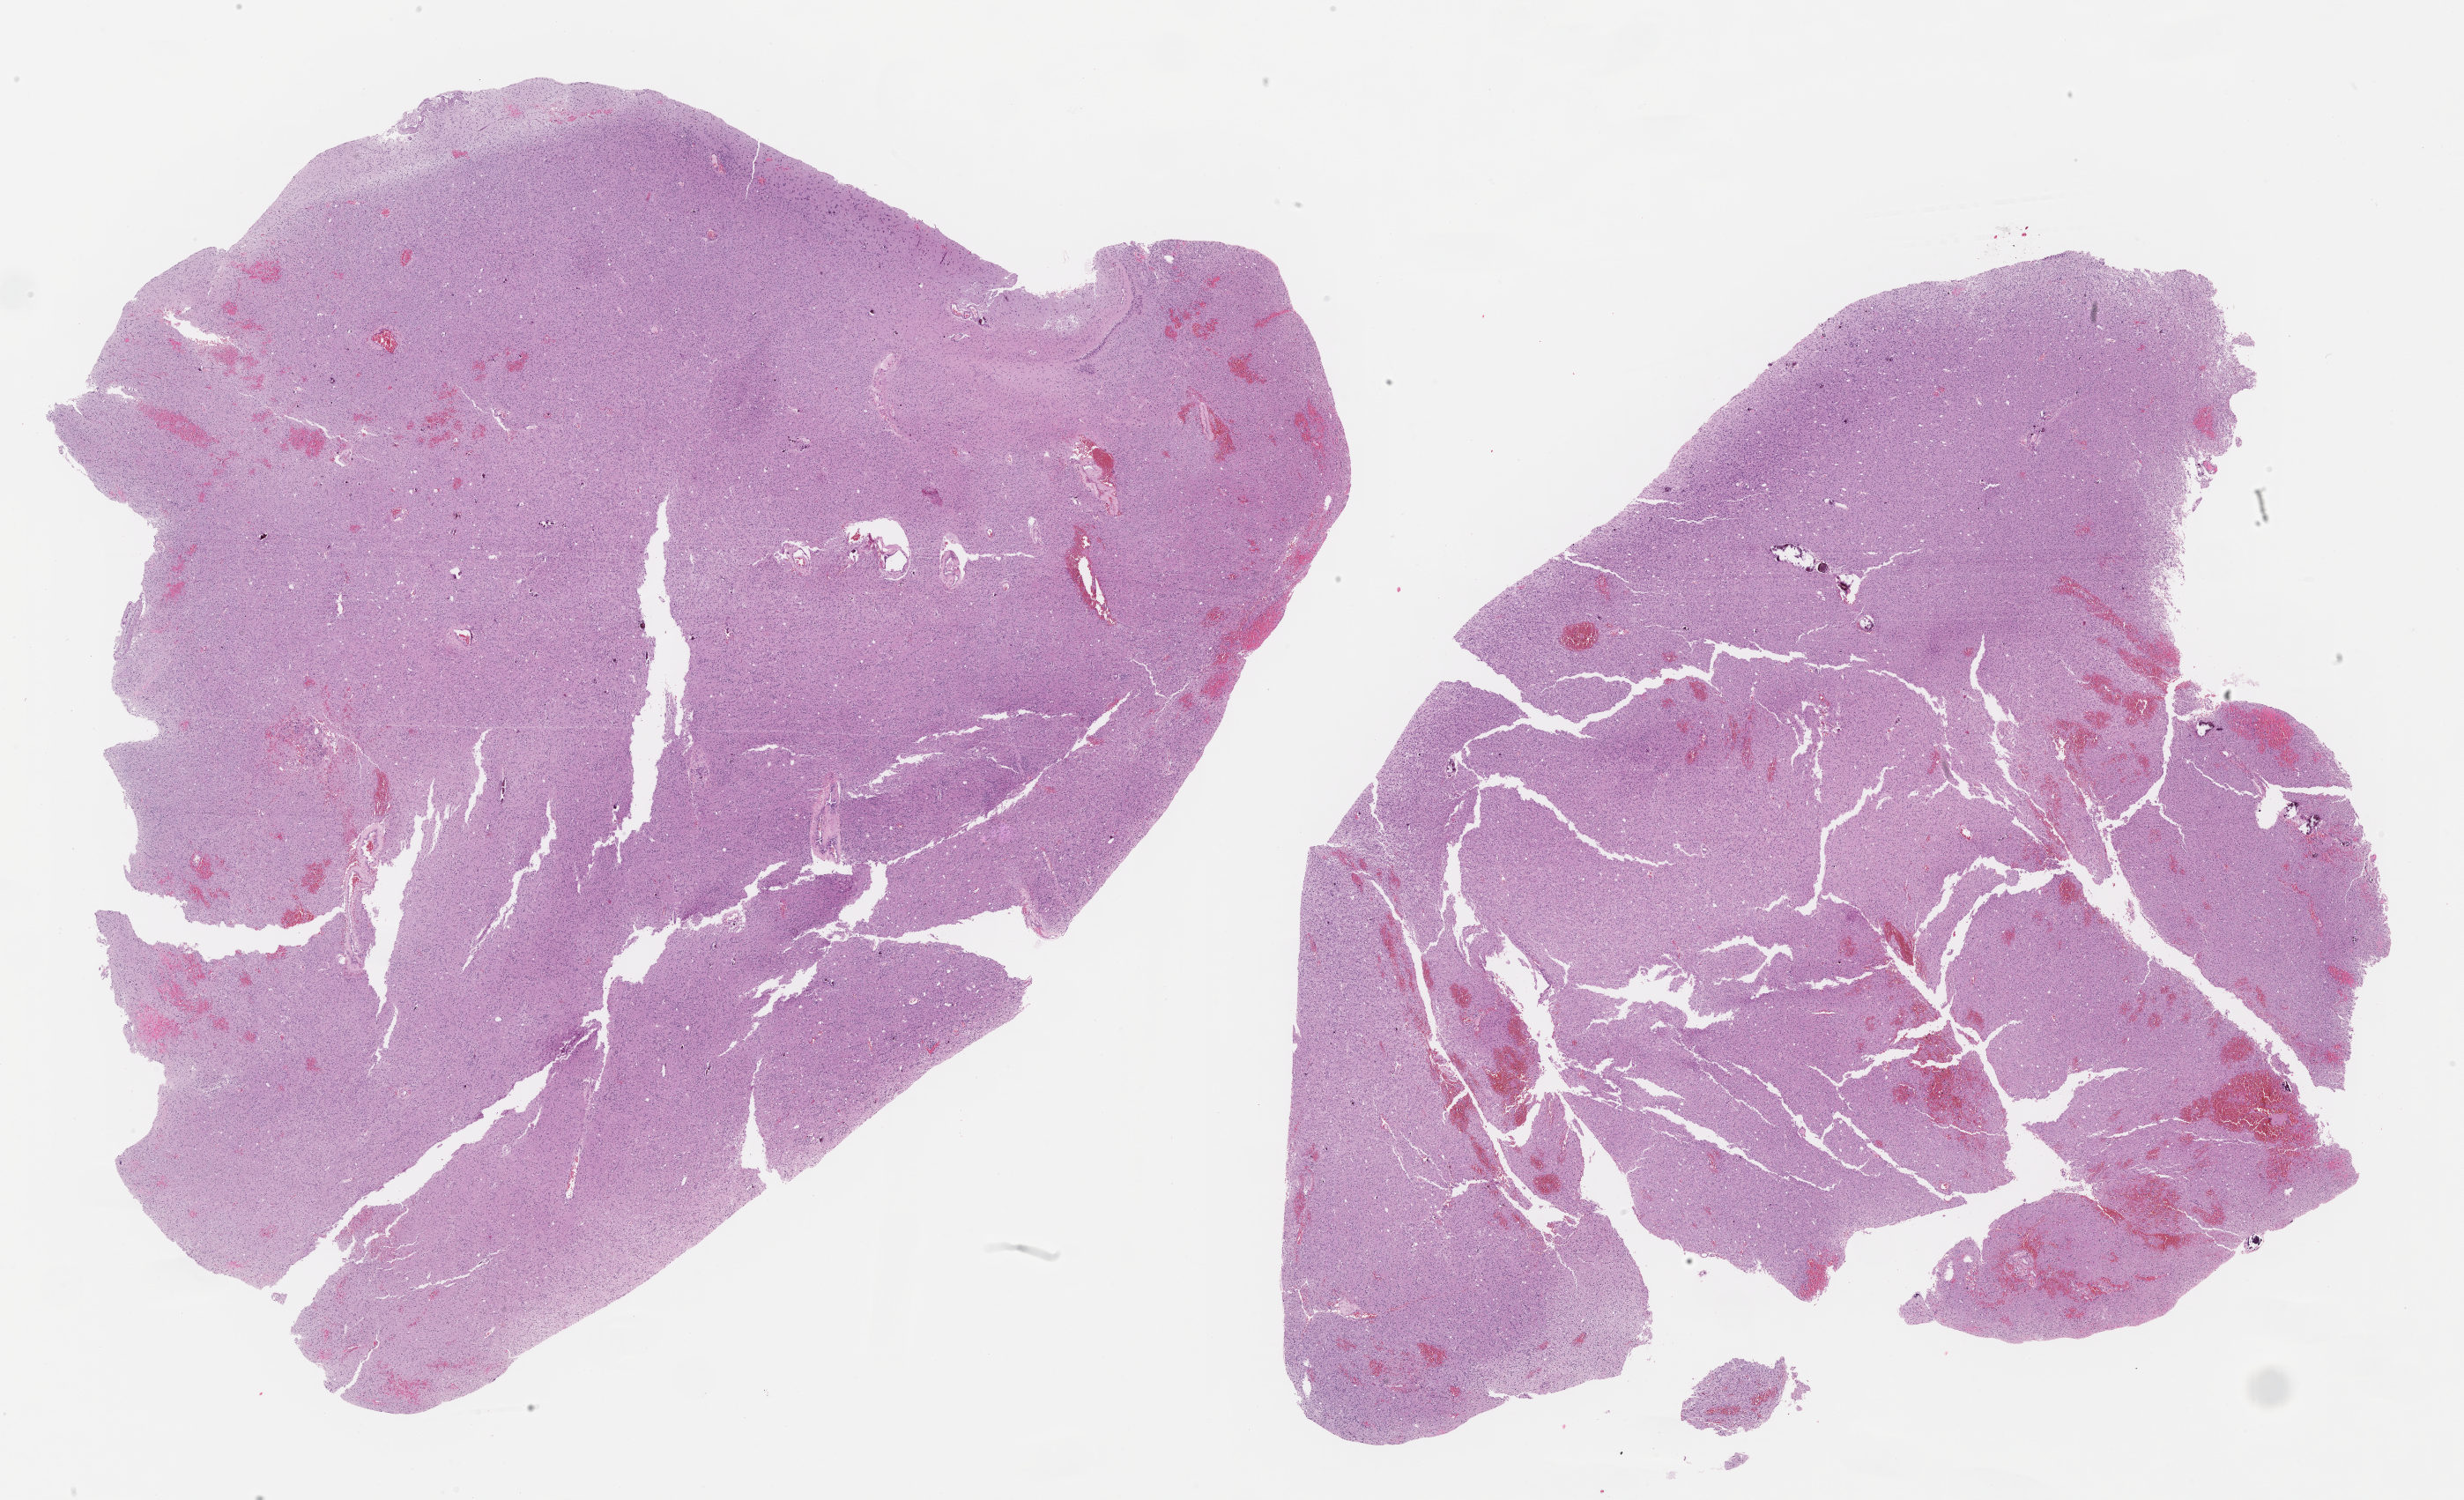
Whole-slide histology image, H&E-stained — shown as a low-resolution overview of the whole scanned area (about 22.5 x 13.7 mm, acquisition: 40x scan); FFPE section; sample: primary tumour, brain. Female patient; age at initial diagnosis 53 years.
Histologic diagnosis: Oligodendroglioma, NOS (cerebrum).